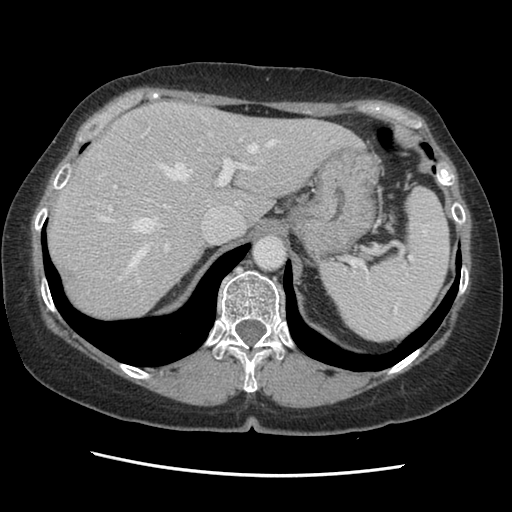
Contrast-enhanced abdominal CT, one axial slice; slice 102 of 141 in the series (ordered by position); 120 kVp; soft-tissue window (W 400 / L 40 HU); 512 × 512 image matrix, field of view 330 × 330 mm. Female patient, age 61 years. Case-level facts recorded for this patient, not image findings: diagnosis: colorectal cancer liver metastases, imaged before liver resection; multiple liver metastases: no; largest metastasis: 2.4 cm.
Annotated regions visible in this slice (outlined manually by an expert reader):
- hepatic veins: bounding box [x1, y1, x2, y2] px = [99, 120, 276, 284]
- liver: [48, 103, 357, 322]
- planned liver remnant (the part of the liver to remain after resection): [48, 103, 357, 322]
- portal vein (with intrahepatic branches): [108, 129, 254, 251]